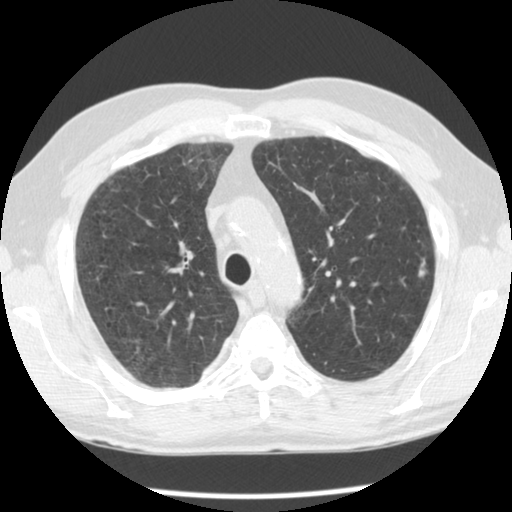
Chest CT (low-dose screening protocol), one axial image, second annual screen, lung window (W 1500 / L -600 HU), 2.5 mm slice thickness. Male participant, aged 59 years at enrolment.
Expert reader's lesion annotation, bounding box (x1, y1, x2, y2) in pixels: (391, 248, 437, 296). The screening reader recorded 2 non-calcified nodules or masses ≥4 mm on this exam (left upper lobe, right upper lobe); which of them this box marks is not recorded.